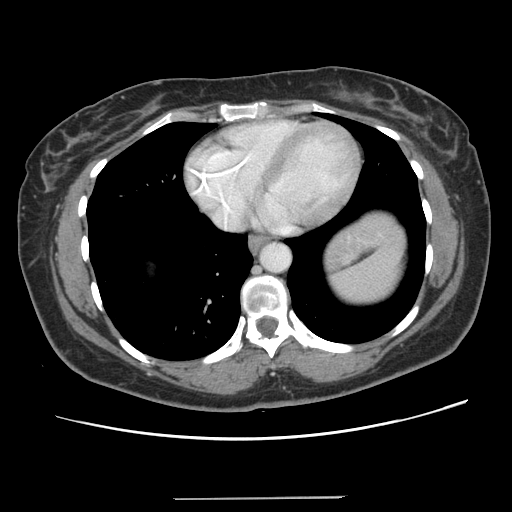
Contrast-enhanced abdominal CT, one axial slice. Slice 128 of 141 in the series (ordered by position). 120 kVp. Intravenous contrast given. Soft-tissue window (W 400 / L 40 HU). 2.5 mm slice thickness. 512 × 512 image matrix. Female patient, age 53 years. Case-level facts recorded for this patient, not image findings: diagnosis: colorectal cancer liver metastases, imaged before liver resection; multiple liver metastases: no; largest metastasis: 14.5 cm; disease in both lobes: yes.
Annotated regions visible in this slice (manually delineated by an expert):
- liver: bounding box <350,212,393,240> (left, top, right, bottom; pixels)